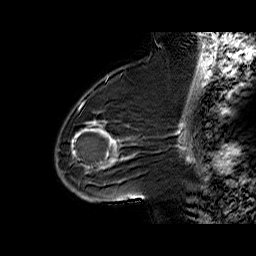
Breast MRI (dynamic contrast-enhanced), one sagittal slice; slice 38 of 60 in the series (ordered by position); dynamic contrast-enhanced series, time point 2 of 6 at this slice position (early post-contrast); 1.5 T; TE 6.3 ms, TR 32.4 ms; 4 mm slice thickness; 256 × 256 image matrix, field of view 200 × 200 mm. Female patient. Case-level facts recorded for this patient, not image findings: setting: breast cancer imaged before/during neoadjuvant chemotherapy; receptor status: triple-negative.
Outlined on this slice (semi-automatically segmented with operator editing):
- analysis volume of interest (the breast-tissue region the enhancement analysis was run in; not a lesion): bounding box [x1, y1, x2, y2] px = [65, 88, 142, 187]
- tumour enhancement mask (voxels above the 100 % enhancement threshold inside the analysis volume of interest): [71, 121, 116, 168]